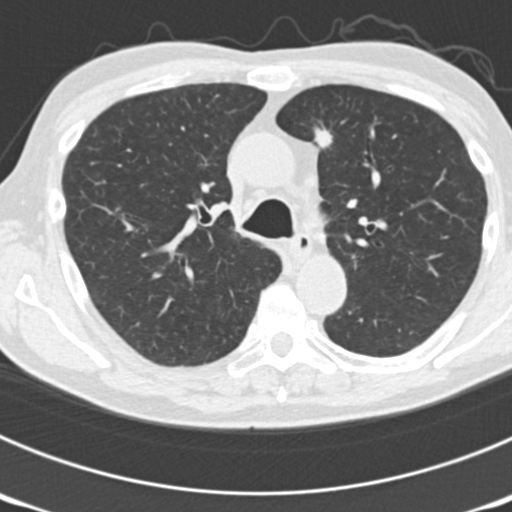
Low-dose screening chest CT, one axial slice; position 125 of 177 along the scan axis; 120 kVp; lung window (W 1500 / L -600 HU); 2 mm slice thickness; 512 × 512 image matrix.
Outlined on this slice (outlined manually by an expert reader):
- lesion 4 (tumor): bounding box [x1, y1, x2, y2] px = [314, 125, 334, 148]